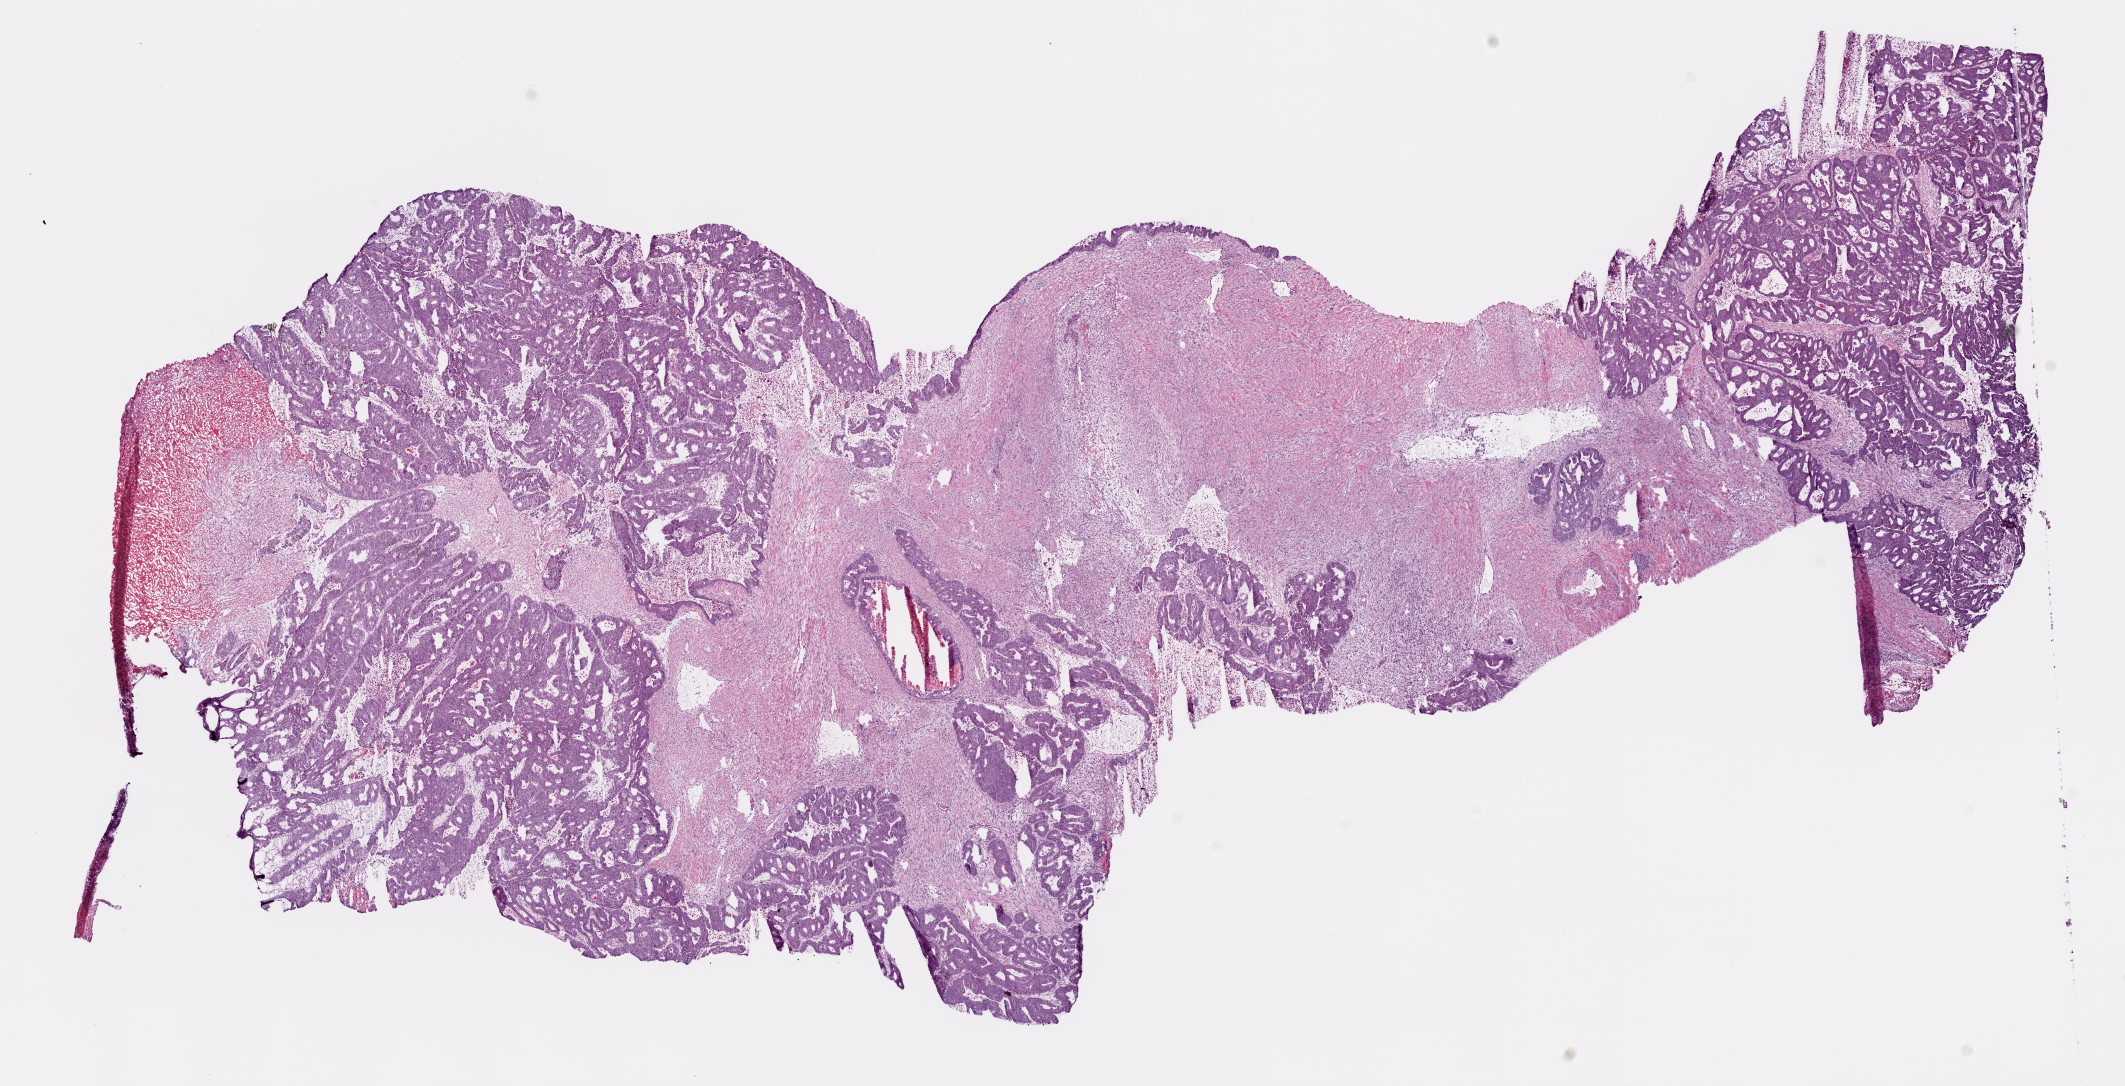
Digitized H&E tissue section (whole slide) — a low-resolution overview of the entire scanned area, about 17.1 x 8.7 mm (slide scanned at 20x), frozen section from the bottom of the tissue portion, sample: primary tumour, colon. Patient: male, age at initial diagnosis 78 years. Composition of this section per pathologist review: tumour cells 80%, tumour nuclei 80%, normal cells 10%, stromal cells 0%, necrosis 10%. Inflammatory infiltration, as recorded: lymphocyte infiltration 5%, monocyte infiltration 1%, neutrophil infiltration 1%.
Histologic diagnosis: Adenocarcinoma, NOS. AJCC pathologic stage: IIC. Lymph nodes positive (case pathology): 0 of 30 examined.